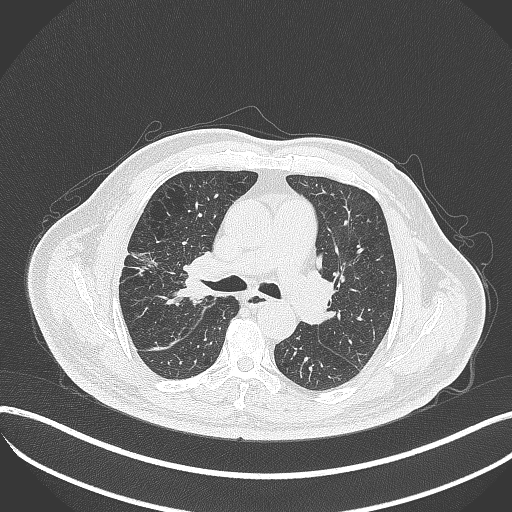
Chest CT, one axial slice; slice 223 of 401 in the series (ordered by position); 120 kVp; lung window (W 1500 / L -600 HU); 1 mm slice thickness; 512 × 512 image matrix, field of view 400 × 400 mm. Male patient, age 72 years. Case-level facts recorded for this patient, not image findings: clinical TNM (as recorded): T1c N0 M0.
Annotated regions visible in this slice (bounding box drawn by a radiologist):
- lung tumour (recorded histology: squamous cell carcinoma): box from (x=165, y=252) to (x=202, y=309) px